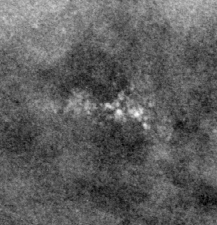
Crop from a digitized film mammogram around one marked abnormality, right breast, CC view.
- Finding: calcifications, morphology pleomorphic, distribution clustered; BI-RADS assessment category 4; subtlety rating 3 on a 1 (subtle) to 5 (obvious) scale; pathology result (as recorded, not read from the image): benign.